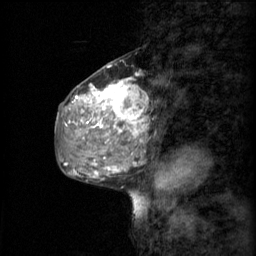
Breast MRI (dynamic contrast-enhanced), one sagittal slice. Slice 27 of 60 in the series (ordered by position). 3 images stored at this slice position (order not interpretable as contrast timing). 1.5 T. TE 4.2 ms, TR 11 ms. 2 mm slice thickness. 256 × 256 image matrix. Female patient, age 48 years.
Annotated regions visible in this slice (semi-automatic segmentation, software-assisted and operator-edited):
- analysis volume of interest (the breast-tissue region the enhancement analysis was run in; not a lesion): bounding box [x1, y1, x2, y2] px = [69, 74, 147, 147]
- tumour enhancement mask (voxels above the 70 % enhancement threshold inside the analysis volume of interest): [73, 78, 147, 141]